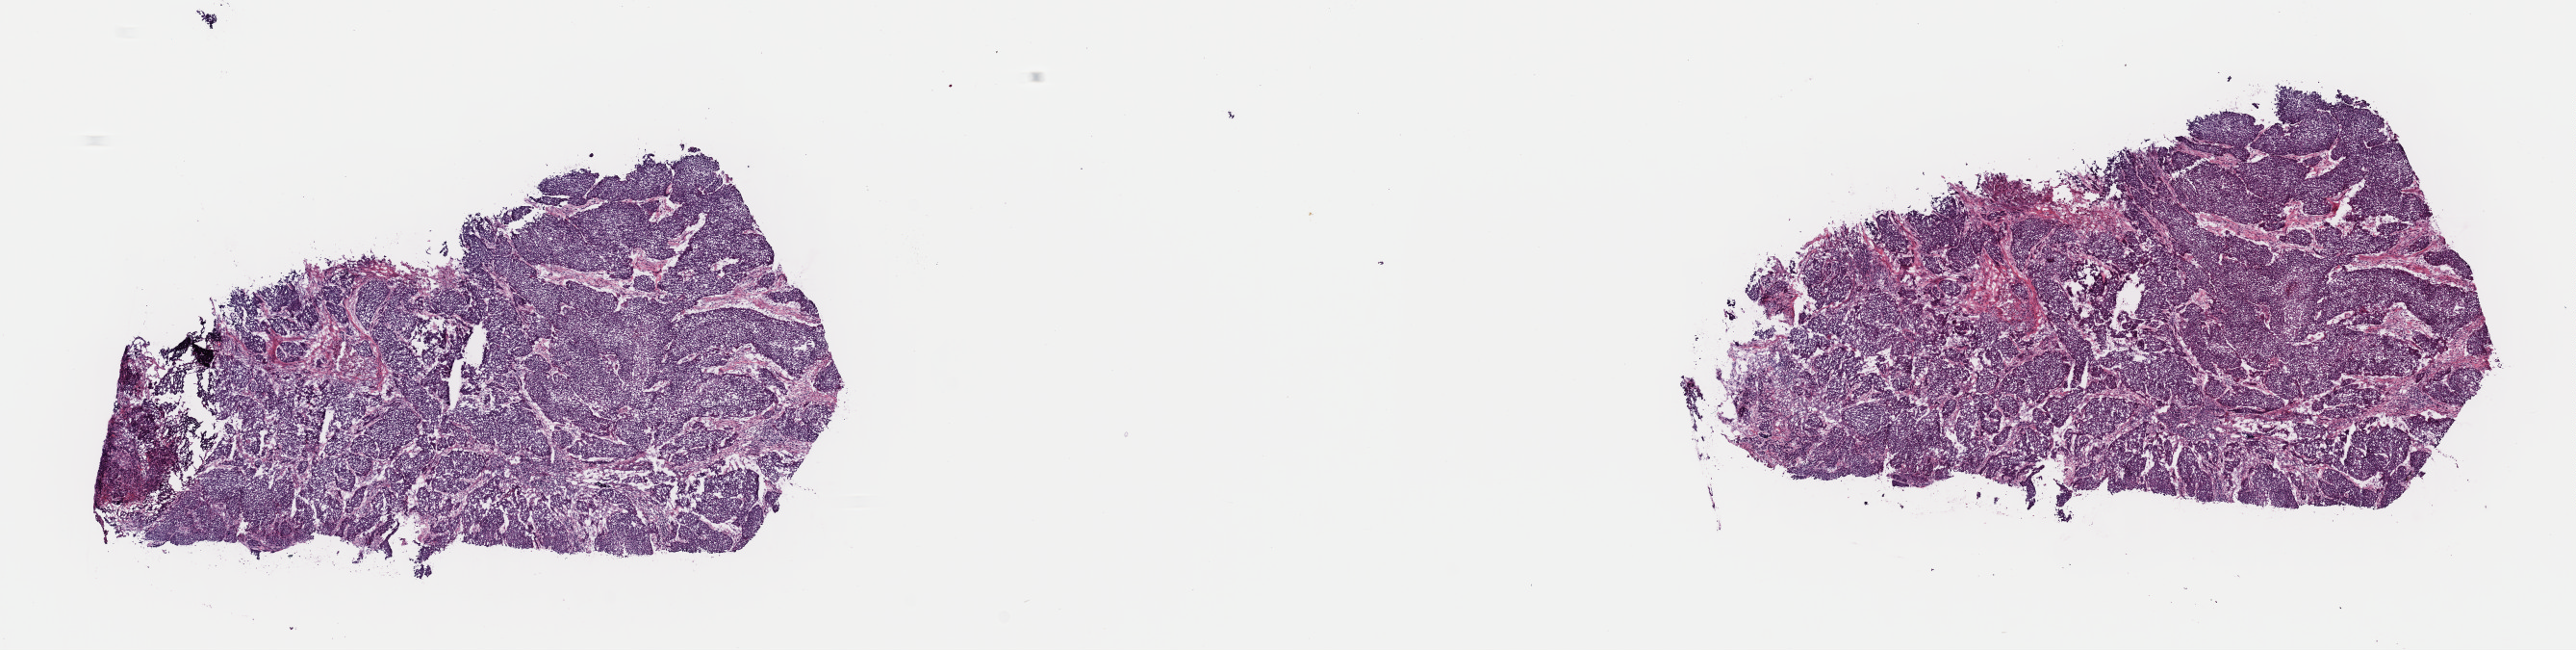
Whole-slide histology image, H&E-stained — whole scanned area (about 21.1 x 5.3 mm) shown as a low-resolution overview; frozen section; sample: primary tumour, head and neck. Male patient; age at initial diagnosis 53 years. Histologic grade: G3 (poorly differentiated). Pathologist review of this section (percent, as recorded): tumour cells 80%, tumour nuclei 95%, normal cells 0%, stromal cells 20%, necrosis 0%. Infiltration values recorded for this section: lymphocyte infiltration 4%, monocyte infiltration 5%, neutrophil infiltration 0%.
- pathologic diagnosis: Squamous cell carcinoma, NOS (lower gum)
- AJCC pathologic stage: IVA
- laterality: right